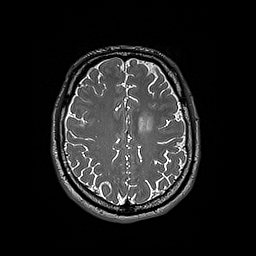
Brain MRI from a brain-tumour surgery series, one axial slice. 1 mm slice thickness. 256 × 256 image matrix. From the clinical record (not read from this slice): histopathology: Oligodendroglioma; WHO grade: 3; IDH mutation: yes; tumour location: Left Frontal.
Annotated regions visible in this slice (outlined manually by an expert reader):
- tumour: bounding box [x1, y1, x2, y2] px = [138, 116, 154, 131]